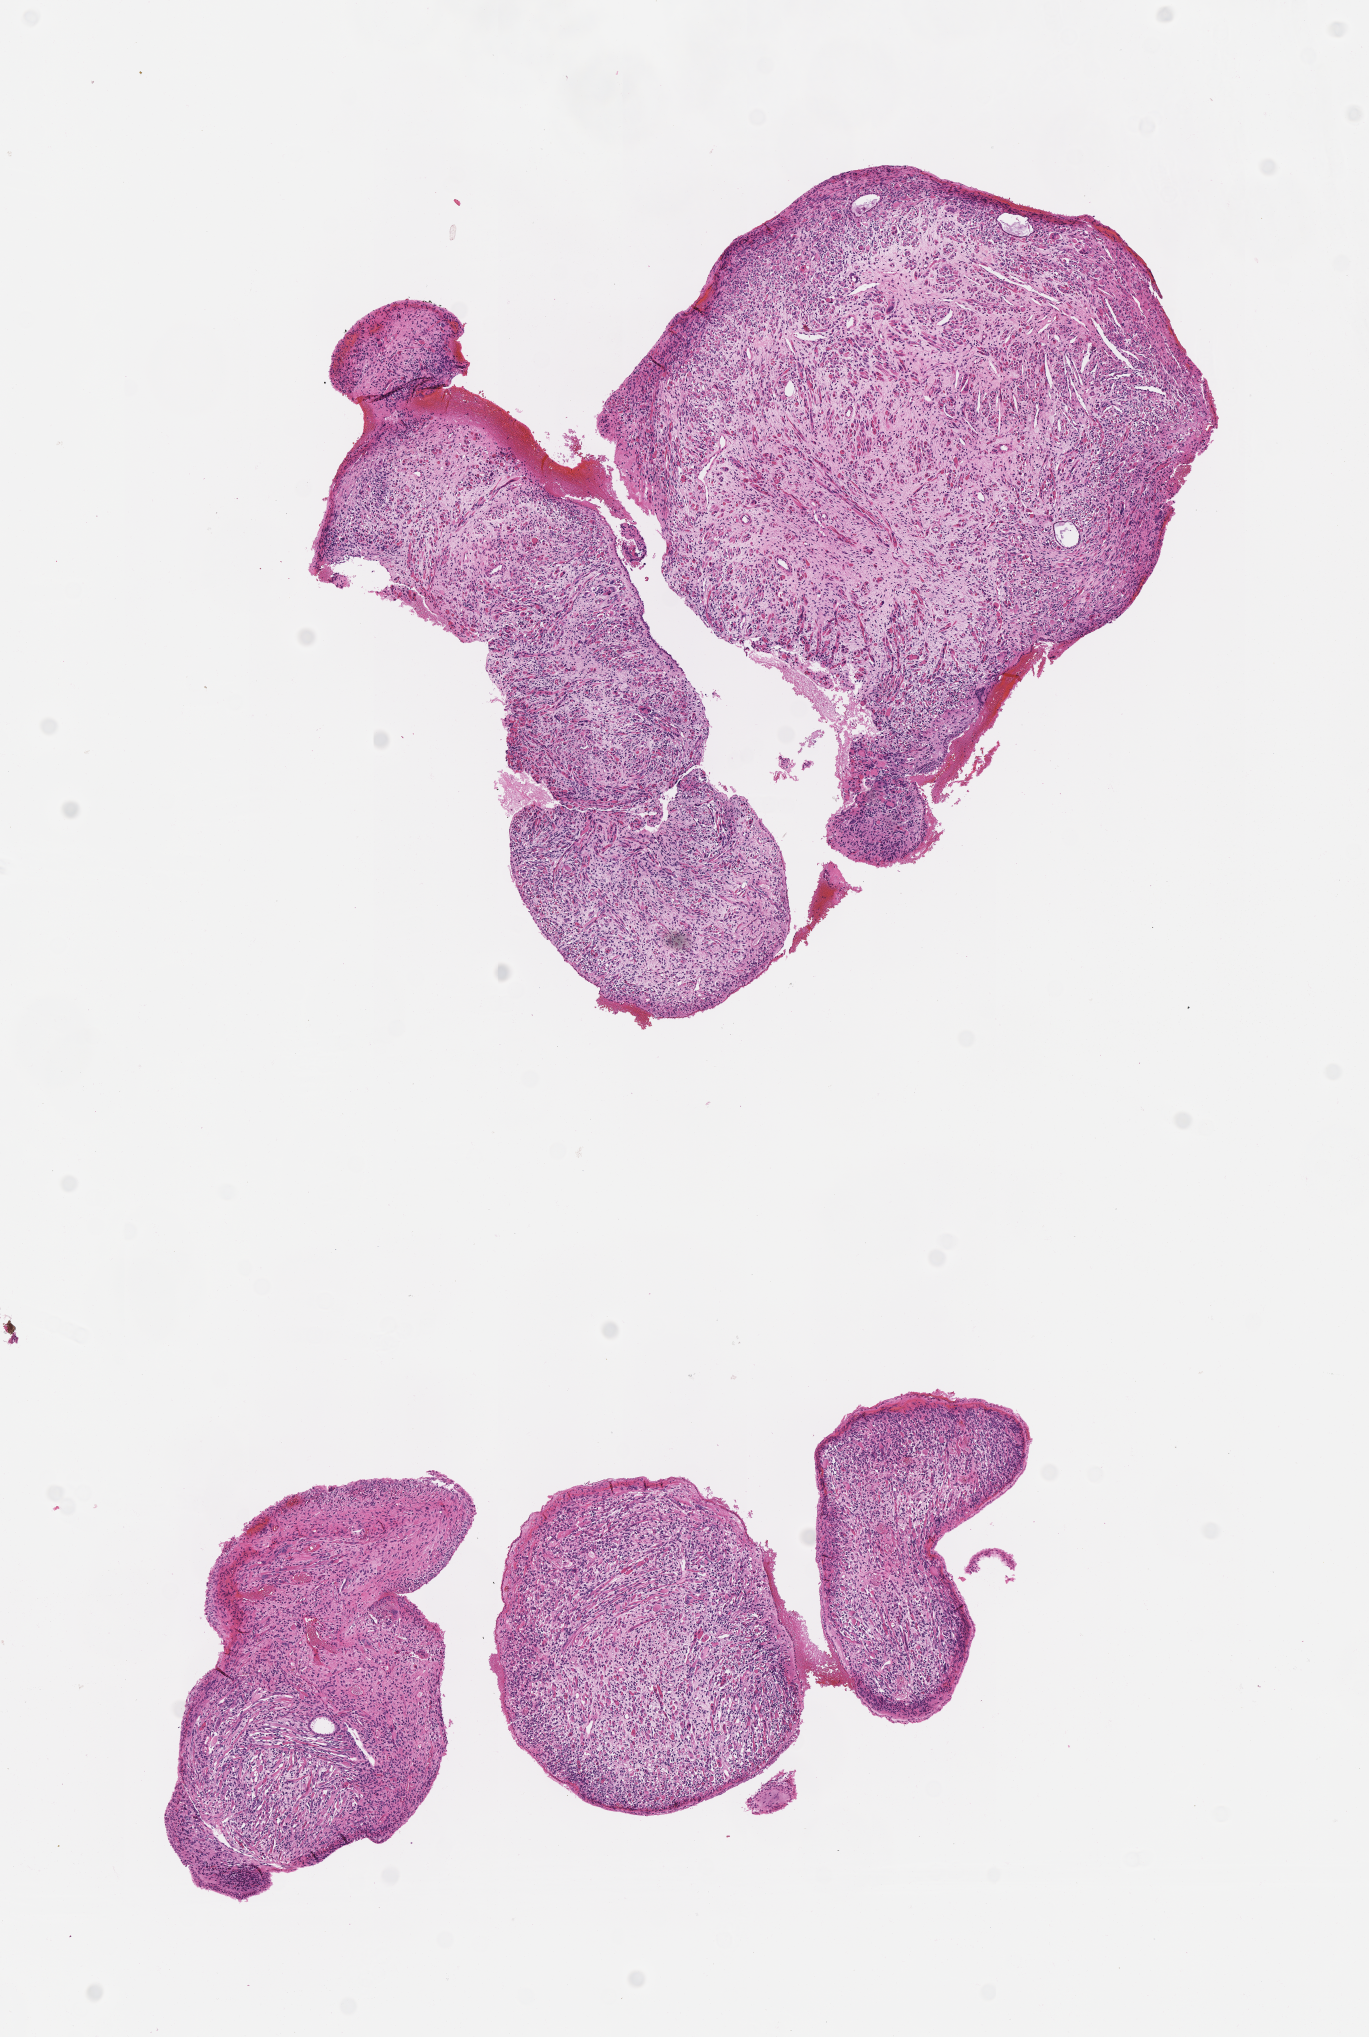
Hematoxylin and eosin (H&E) whole-slide image of tumor tissue, shown as a low-resolution overview of the whole scanned area (about 5.5 x 8.2 mm), formalin-fixed, paraffin-embedded (FFPE) tissue, site: soft tissue, ear-right. Female patient, age at diagnosis 4.4 years.
Diagnosis: rhabdomyosarcoma; histological classification: embryonal rhabdomyosarcoma. Stage (as recorded): 3.